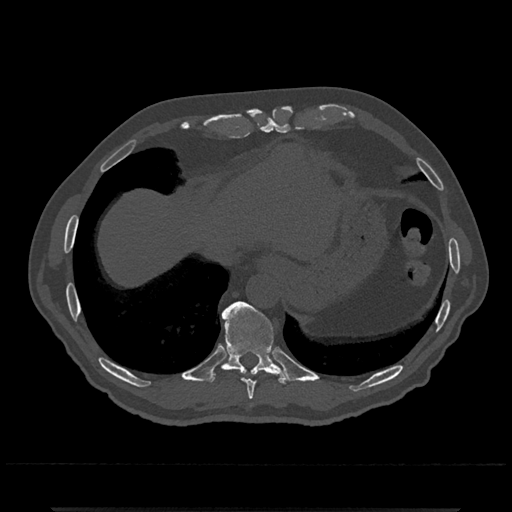
CT including the spine, one axial slice; position 576 of 797 along the scan axis; reconstruction kernel Br40s/3; bone window (W 1800 / L 400 HU); 0.5 mm slice thickness; 512 × 512 image matrix, field of view 393 × 393 mm. Male patient, age 67 years. Case-level facts recorded for this patient, not image findings: primary cancer: prostate.
Outlined on this slice (semi-automatic segmentation, software-assisted and operator-edited):
- T10 vertebra: box from (x=210, y=301) to (x=289, y=385) px
- T9 vertebra: (x=243, y=378)–(x=255, y=400)